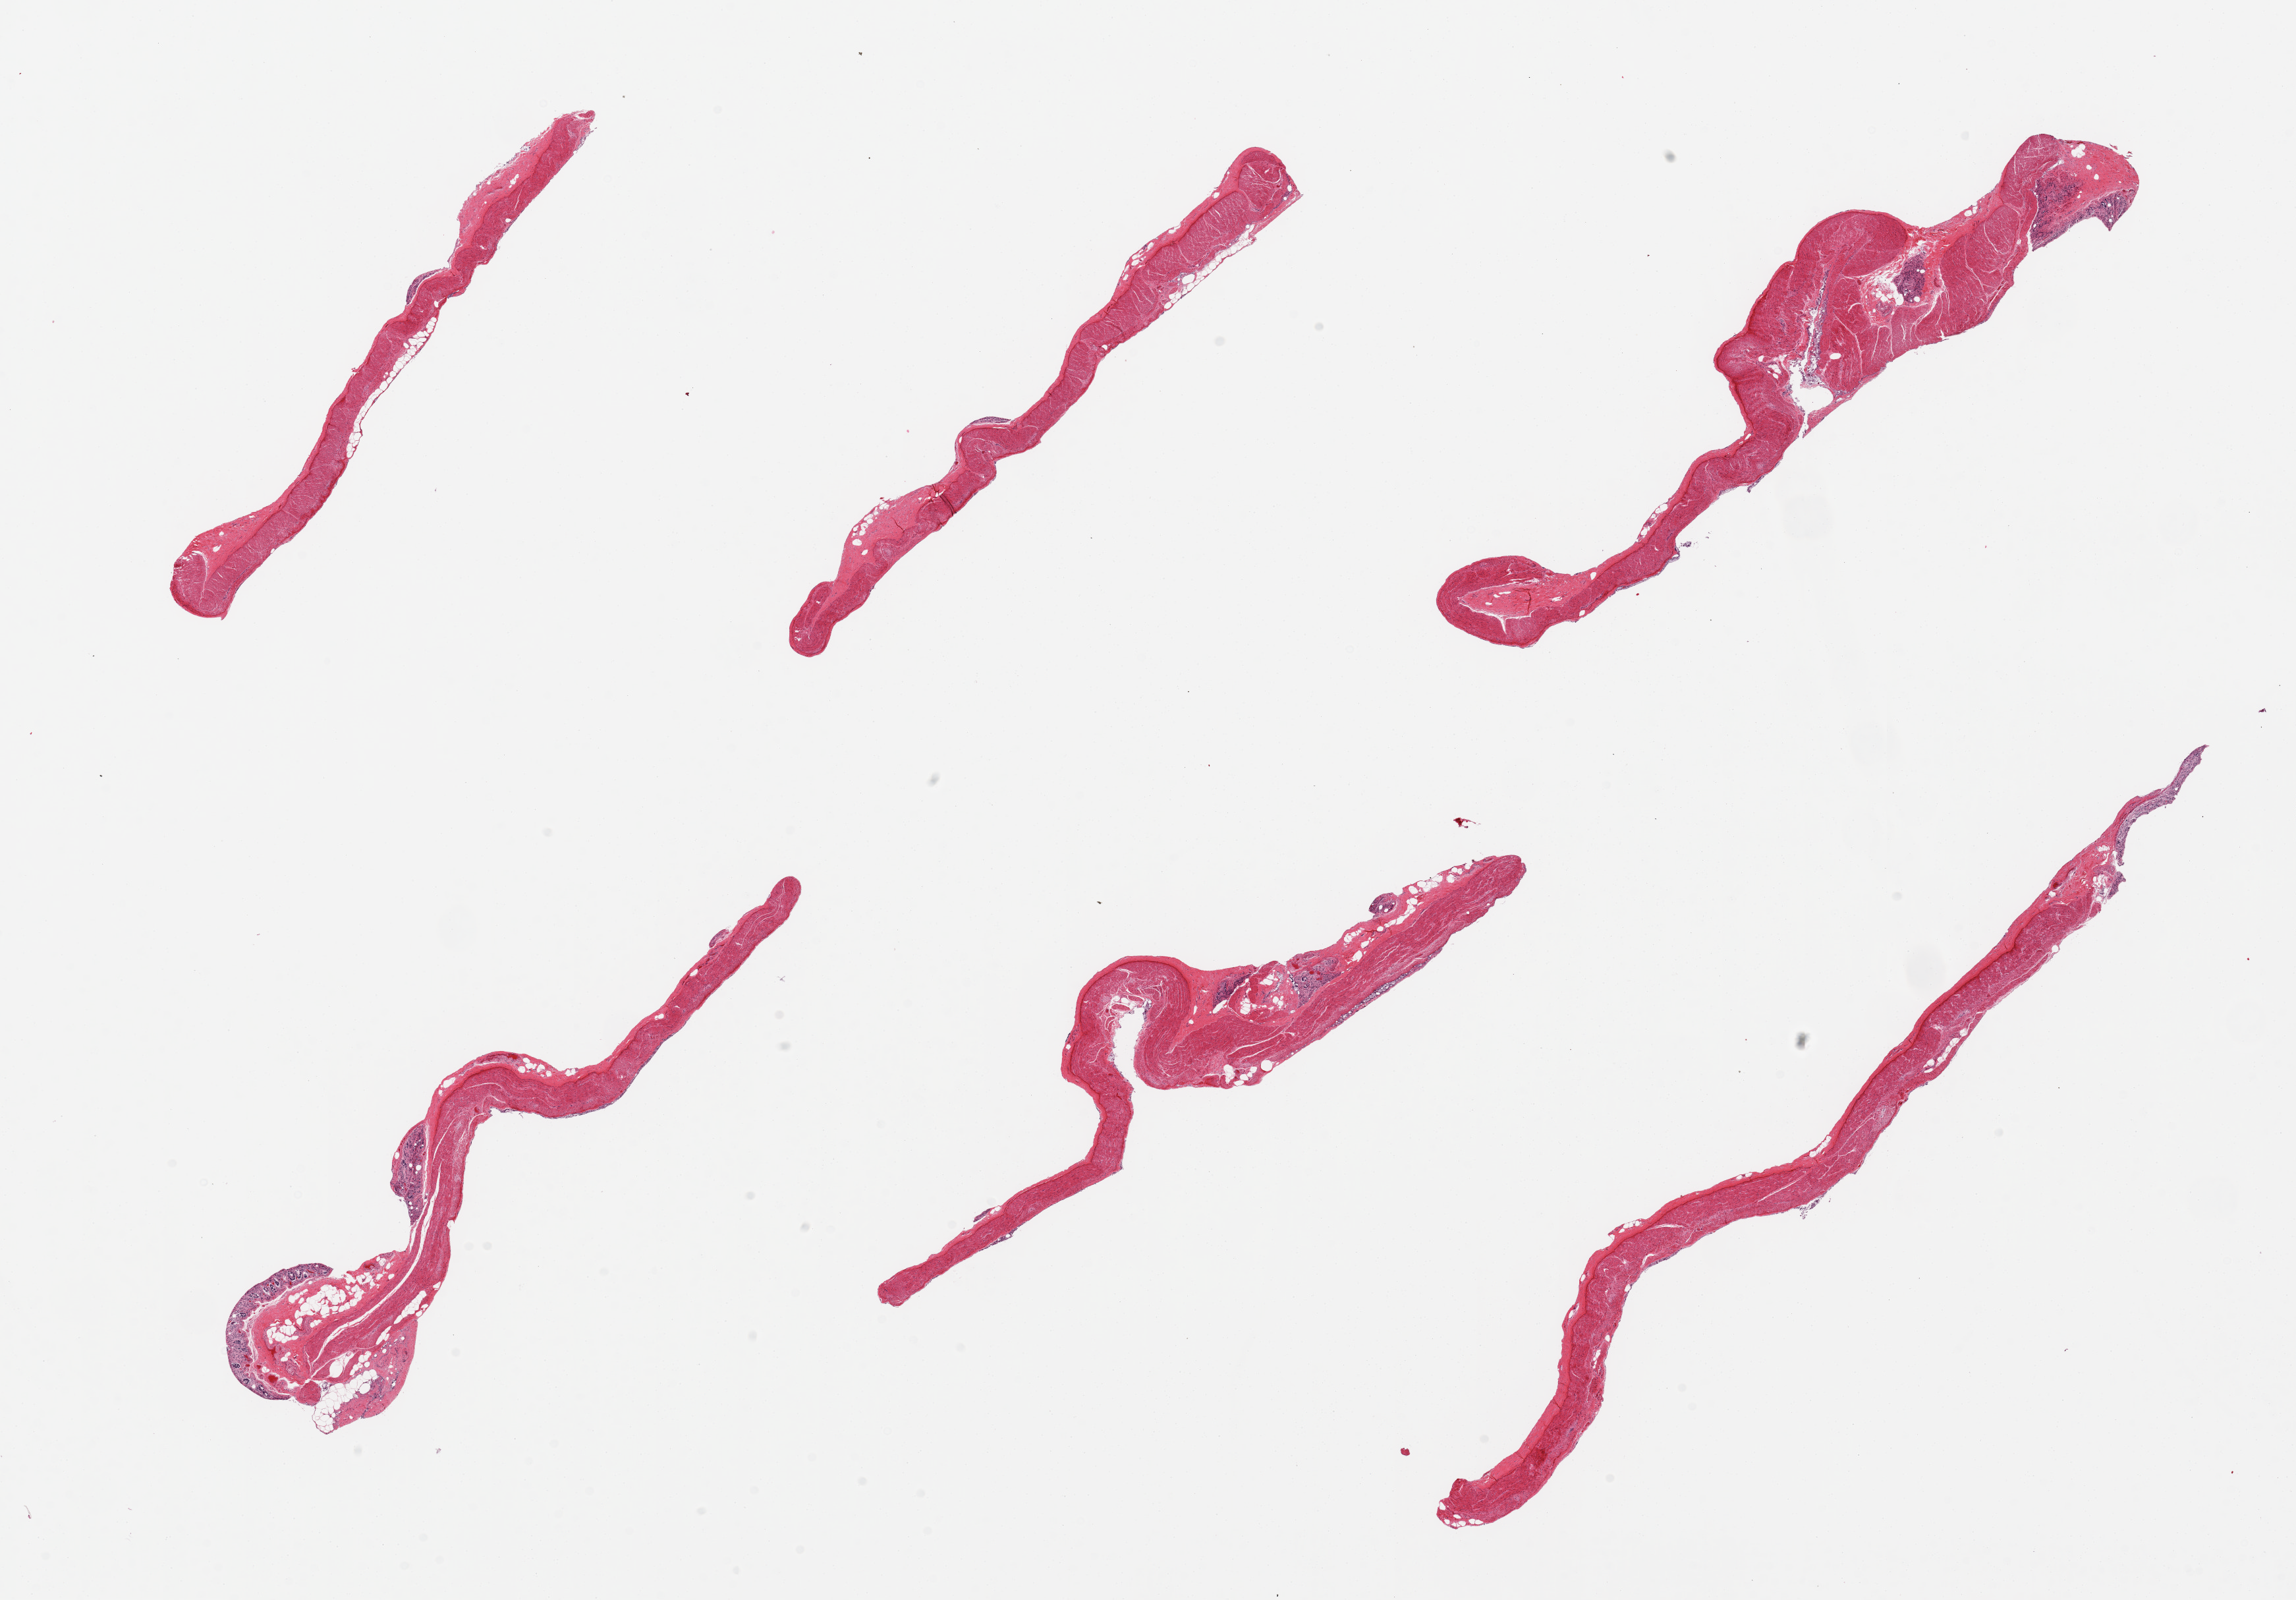
Whole-slide image, H&E stain, brightfield, a low-resolution overview of the entire scanned area, about 27.6 x 19.2 mm, PAXgene-fixed paraffin-embedded (PFPE) section, target tissue: transverse colon, donor tissue sample. Donor: male.
Review note (as recorded): 6 pieces; mucosa completely autolyzed; muscularis intact and mildly autolyzed.